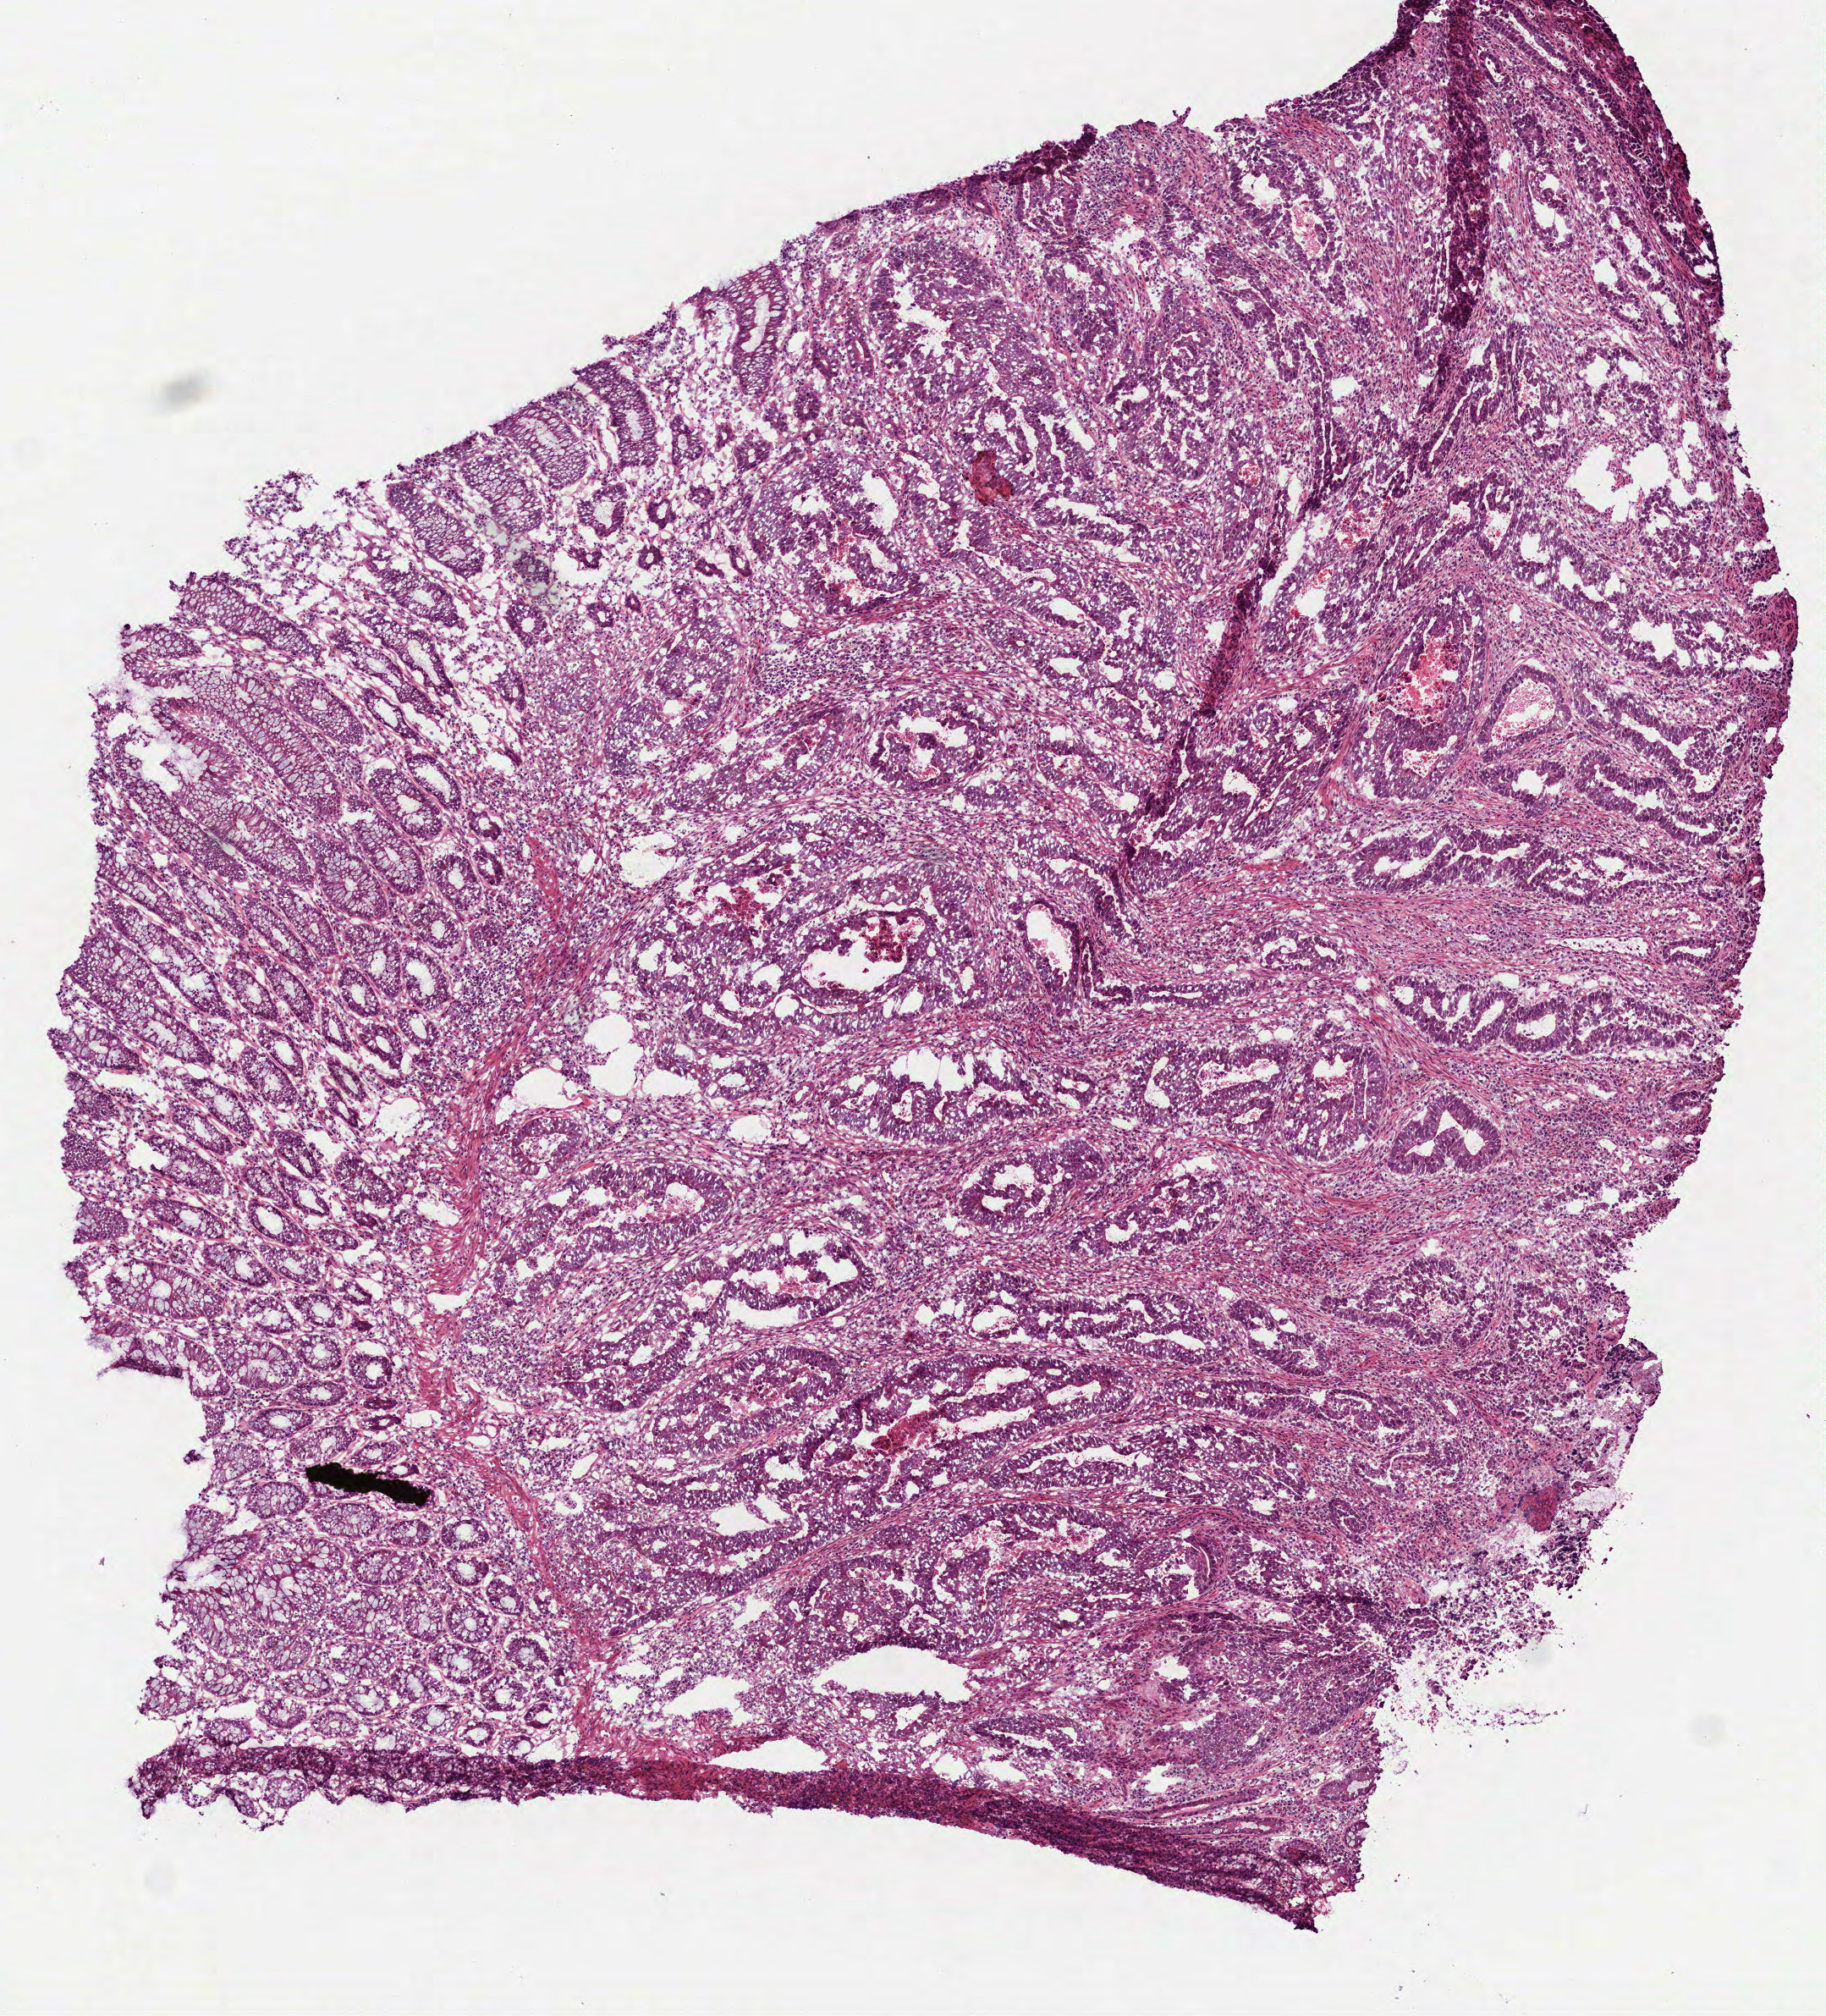
Digitized H&E tissue section (whole slide) — whole scanned area (about 4.4 x 4.8 mm, acquisition: 40x scan) shown as a low-resolution overview. Frozen section from the bottom of the tissue portion. Sample: primary tumour, colon. Patient: male, age at initial diagnosis 77 years.
Pathologic diagnosis: Adenocarcinoma, NOS (ascending colon).